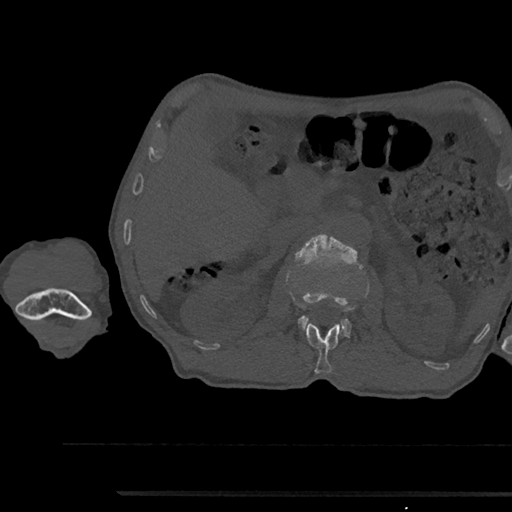
CT including the spine, one axial slice. Position 608 of 797 along the scan axis. Reconstruction kernel Br40s/3. Bone window (W 1800 / L 400 HU). 0.5 mm slice thickness. 512 × 512 image matrix, field of view 367 × 367 mm. Male patient, age 79 years. From the clinical record (not read from this slice): primary cancer: prostate.
Structures marked on this image (semi-automatic segmentation, software-assisted and operator-edited):
- L1 vertebra: bounding box [x1, y1, x2, y2] px = [306, 323, 340, 374]
- L2 vertebra: [295, 234, 369, 338]